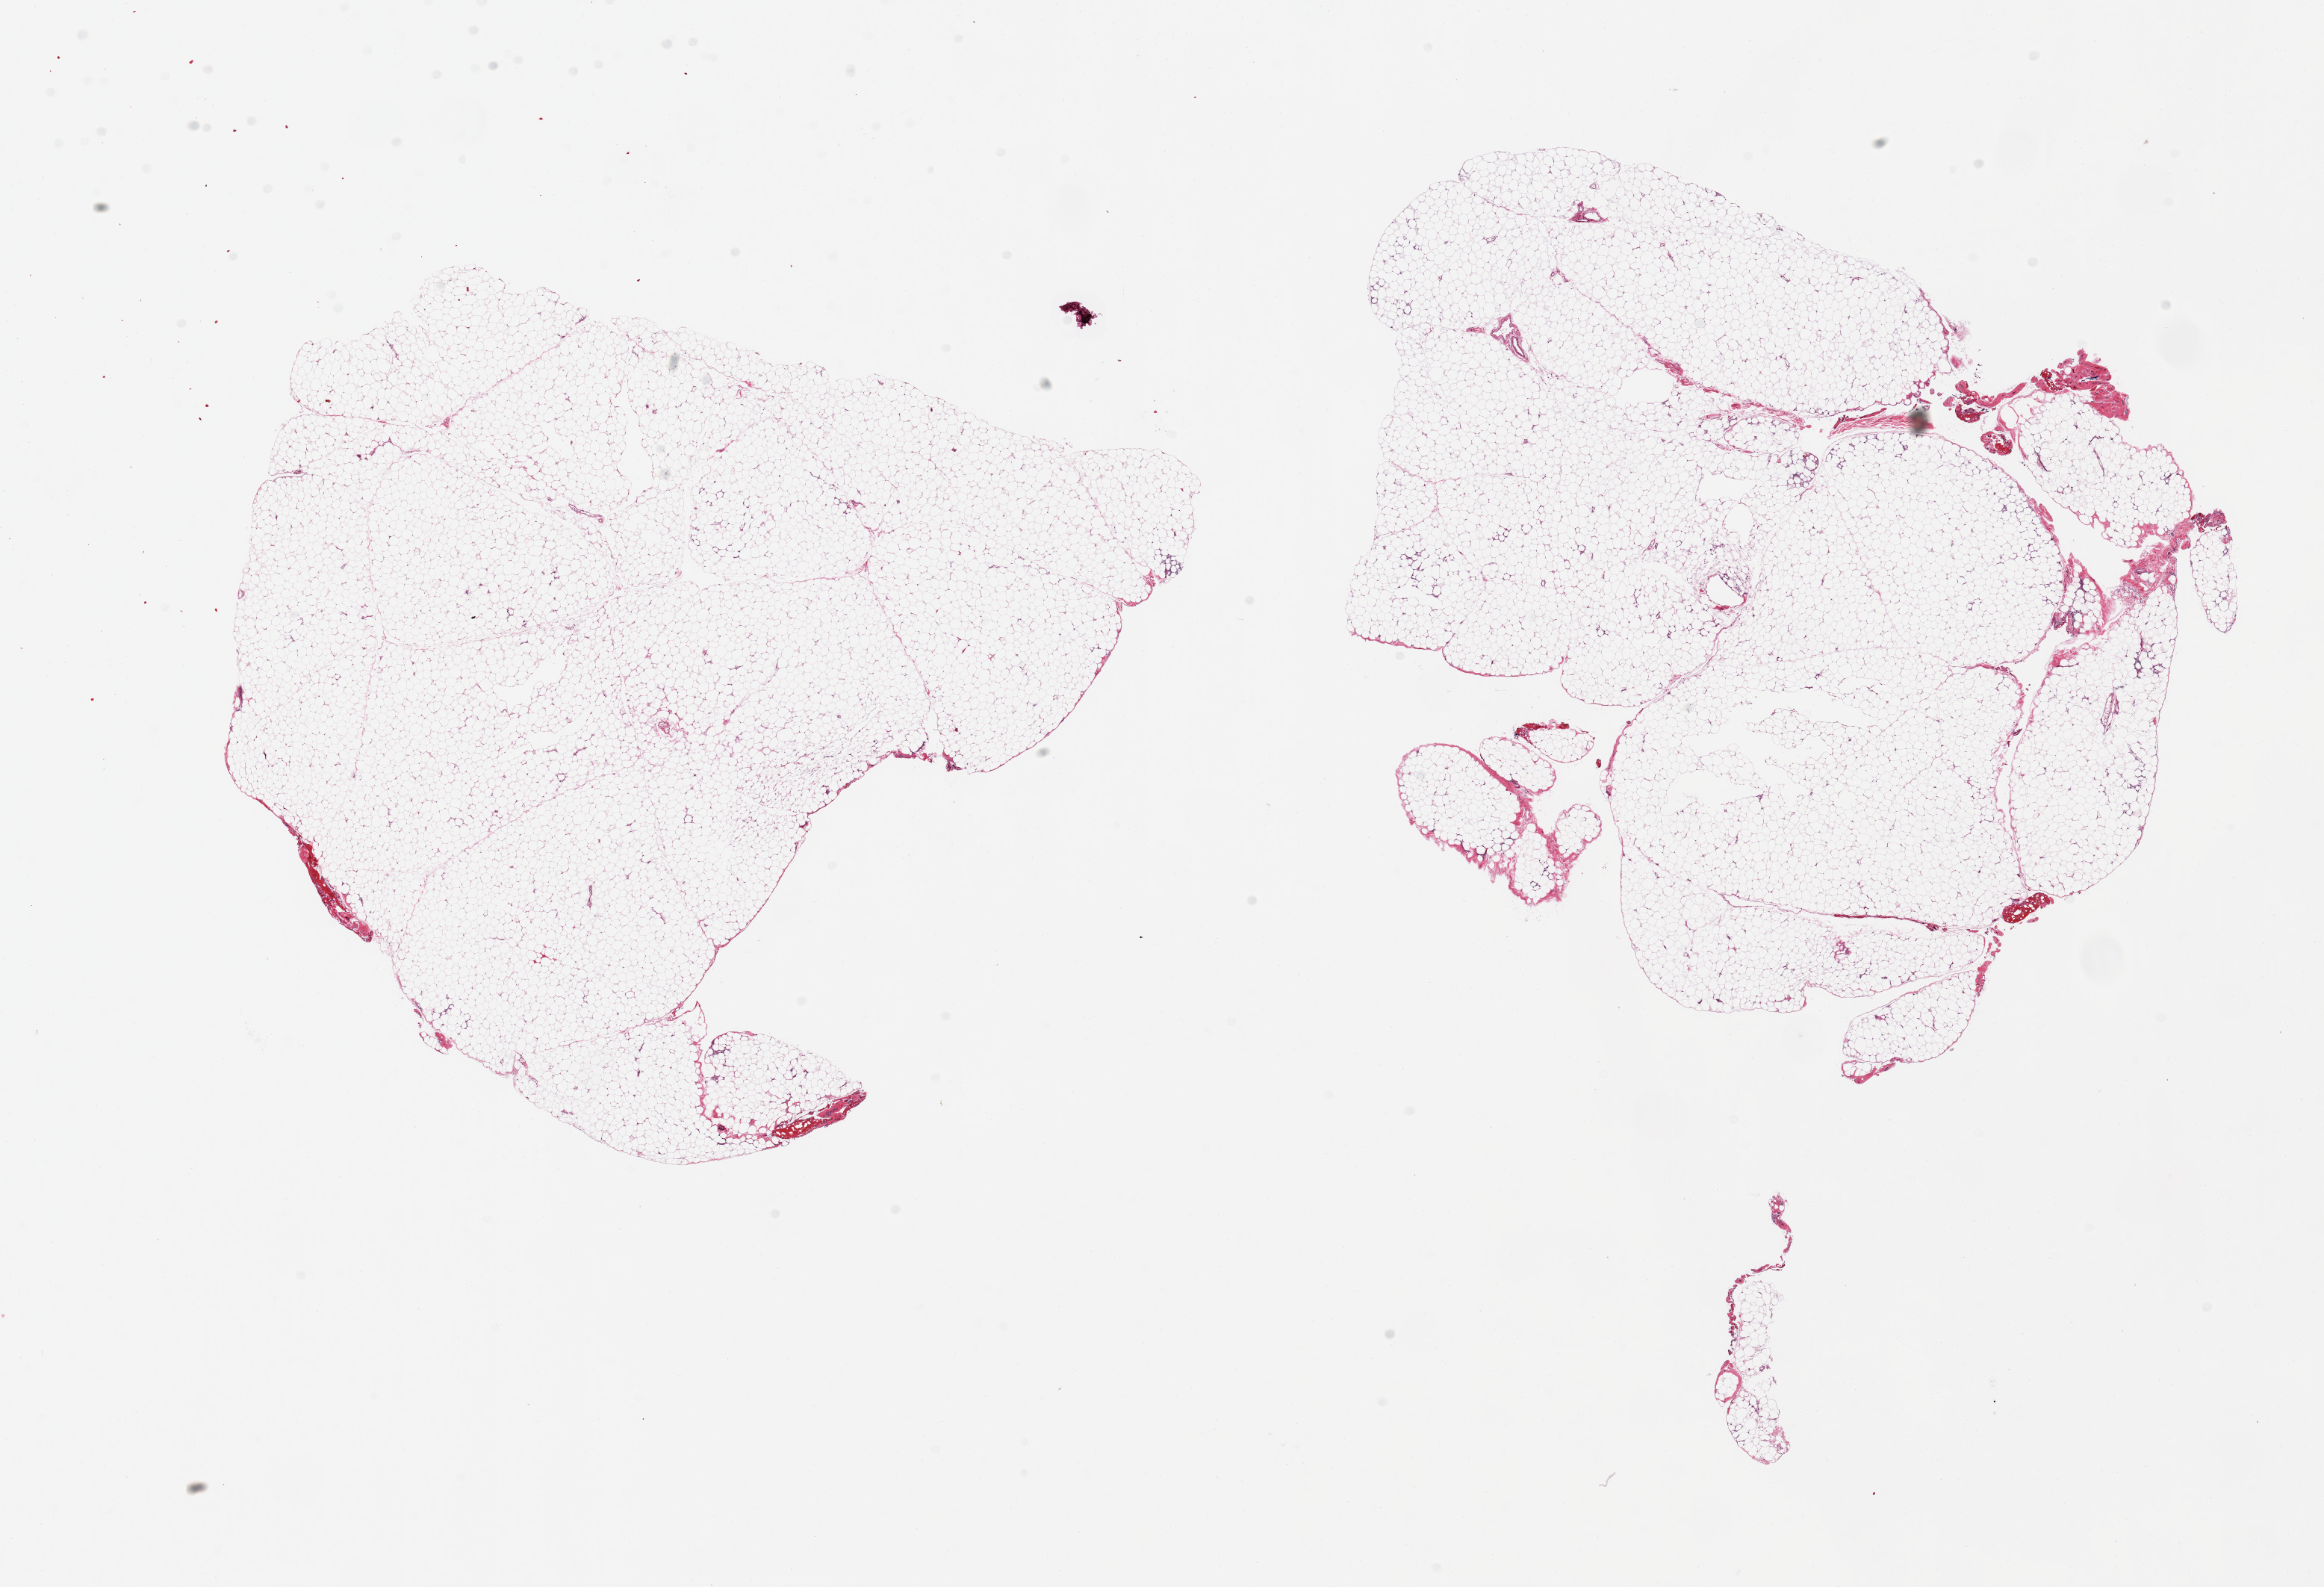
Whole-slide image, hematoxylin and eosin (H&E) stain — whole scanned area (about 24.6 x 16.8 mm) shown as a low-resolution overview. PAXgene-fixed paraffin-embedded (PFPE) section. Section of omentum (target tissue). Donor tissue sample. Male donor.
Reviewer comment on this tissue sample: 2 pieces, trace fascia/vascular elements.